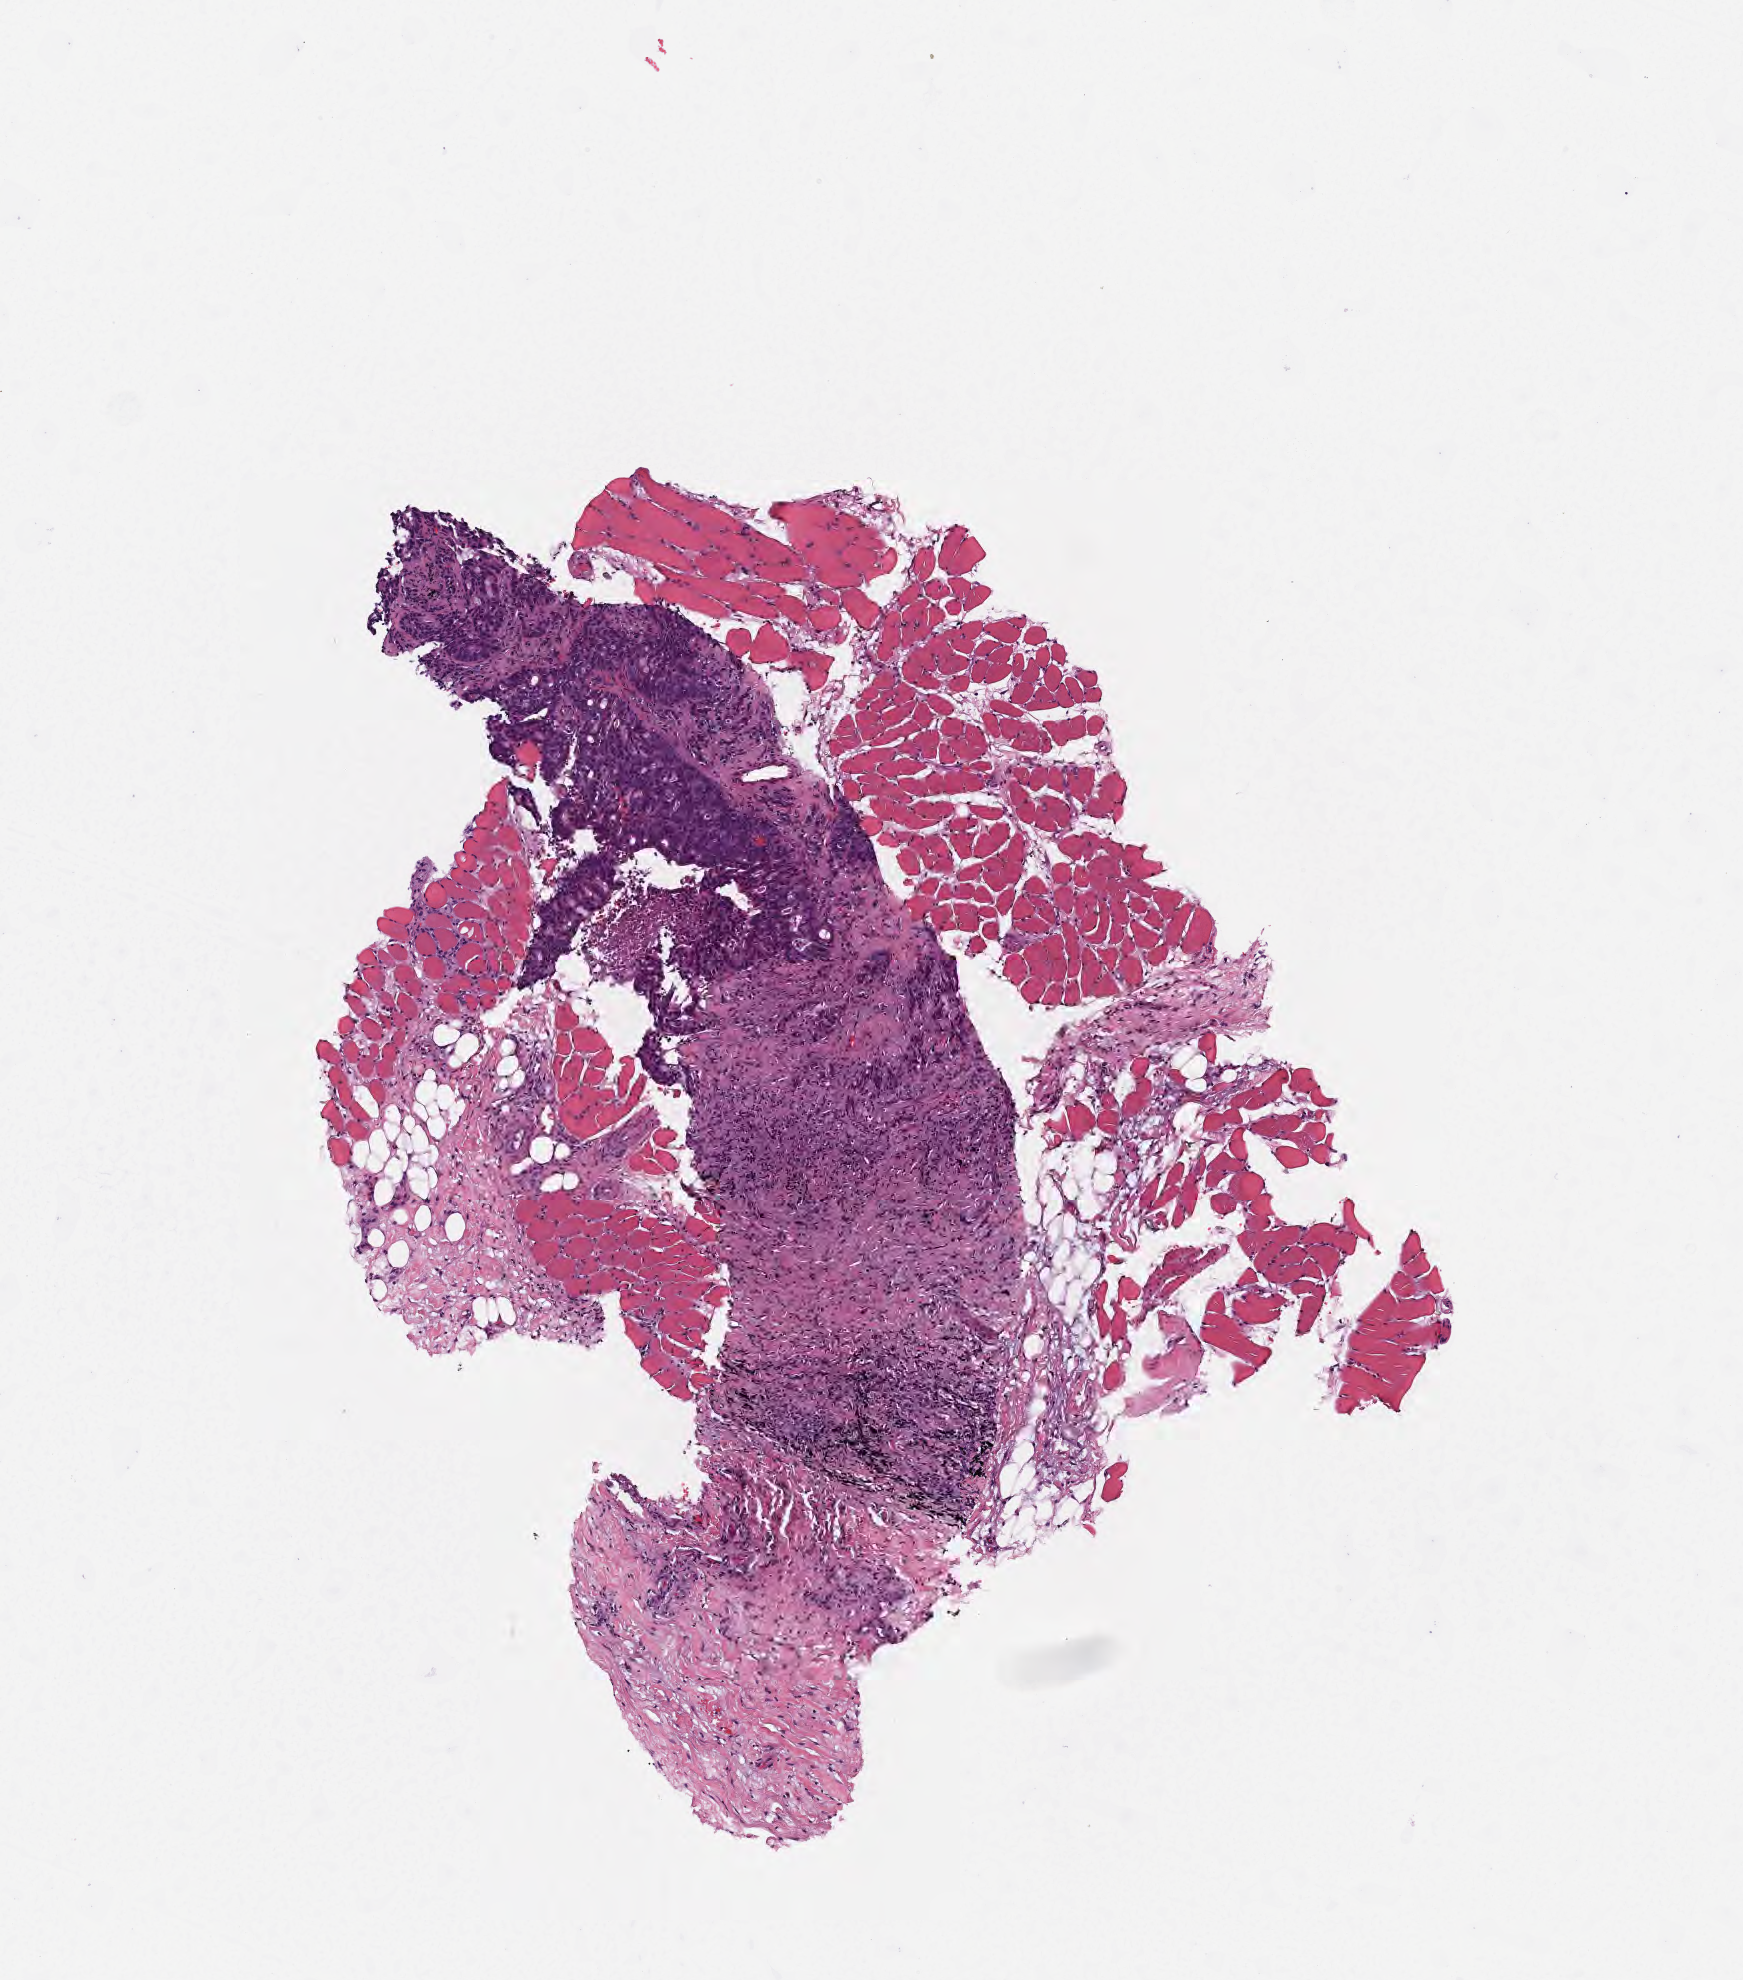
Digitized hematoxylin and eosin (H&E)-stained section — shown as a low-resolution overview of the whole scanned area (about 3.5 x 4.0 mm); tumor tissue; site: lung. Patient female; 68 years old.
- histologic diagnosis: Squamous cell carcinoma, large cell, nonkeratinizing, NOS